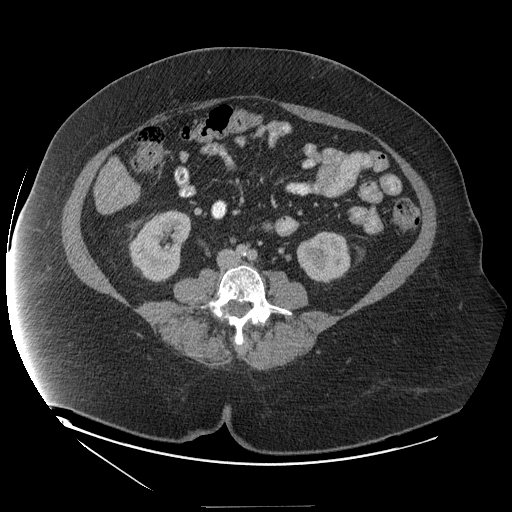
Contrast-enhanced abdominal CT (liver protocol), one axial slice. Slice 24 of 127 in the series (ordered by position). Reconstruction kernel STANDARD. Soft-tissue window (W 400 / L 40 HU). 2.5 mm slice thickness. 512 × 512 image matrix, field of view 480 × 480 mm. Case-level facts recorded for this patient, not image findings: diagnosis: hepatocellular carcinoma (patient treated with transarterial chemoembolisation; whether this scan precedes or follows treatment is not stated here); TNM stage (as recorded): Stage-II; Child-Pugh class: A; tumour differentiation: well differentiated; tumour nodularity: multinodular.
Annotated regions visible in this slice (semi-automatic segmentation, software-assisted and operator-edited):
- liver parenchyma outside the tumour (the mass and vessels are separate outlines, so this box may not span the whole liver): bounding box (x1, y1, x2, y2) in pixels: (94, 159, 132, 214)